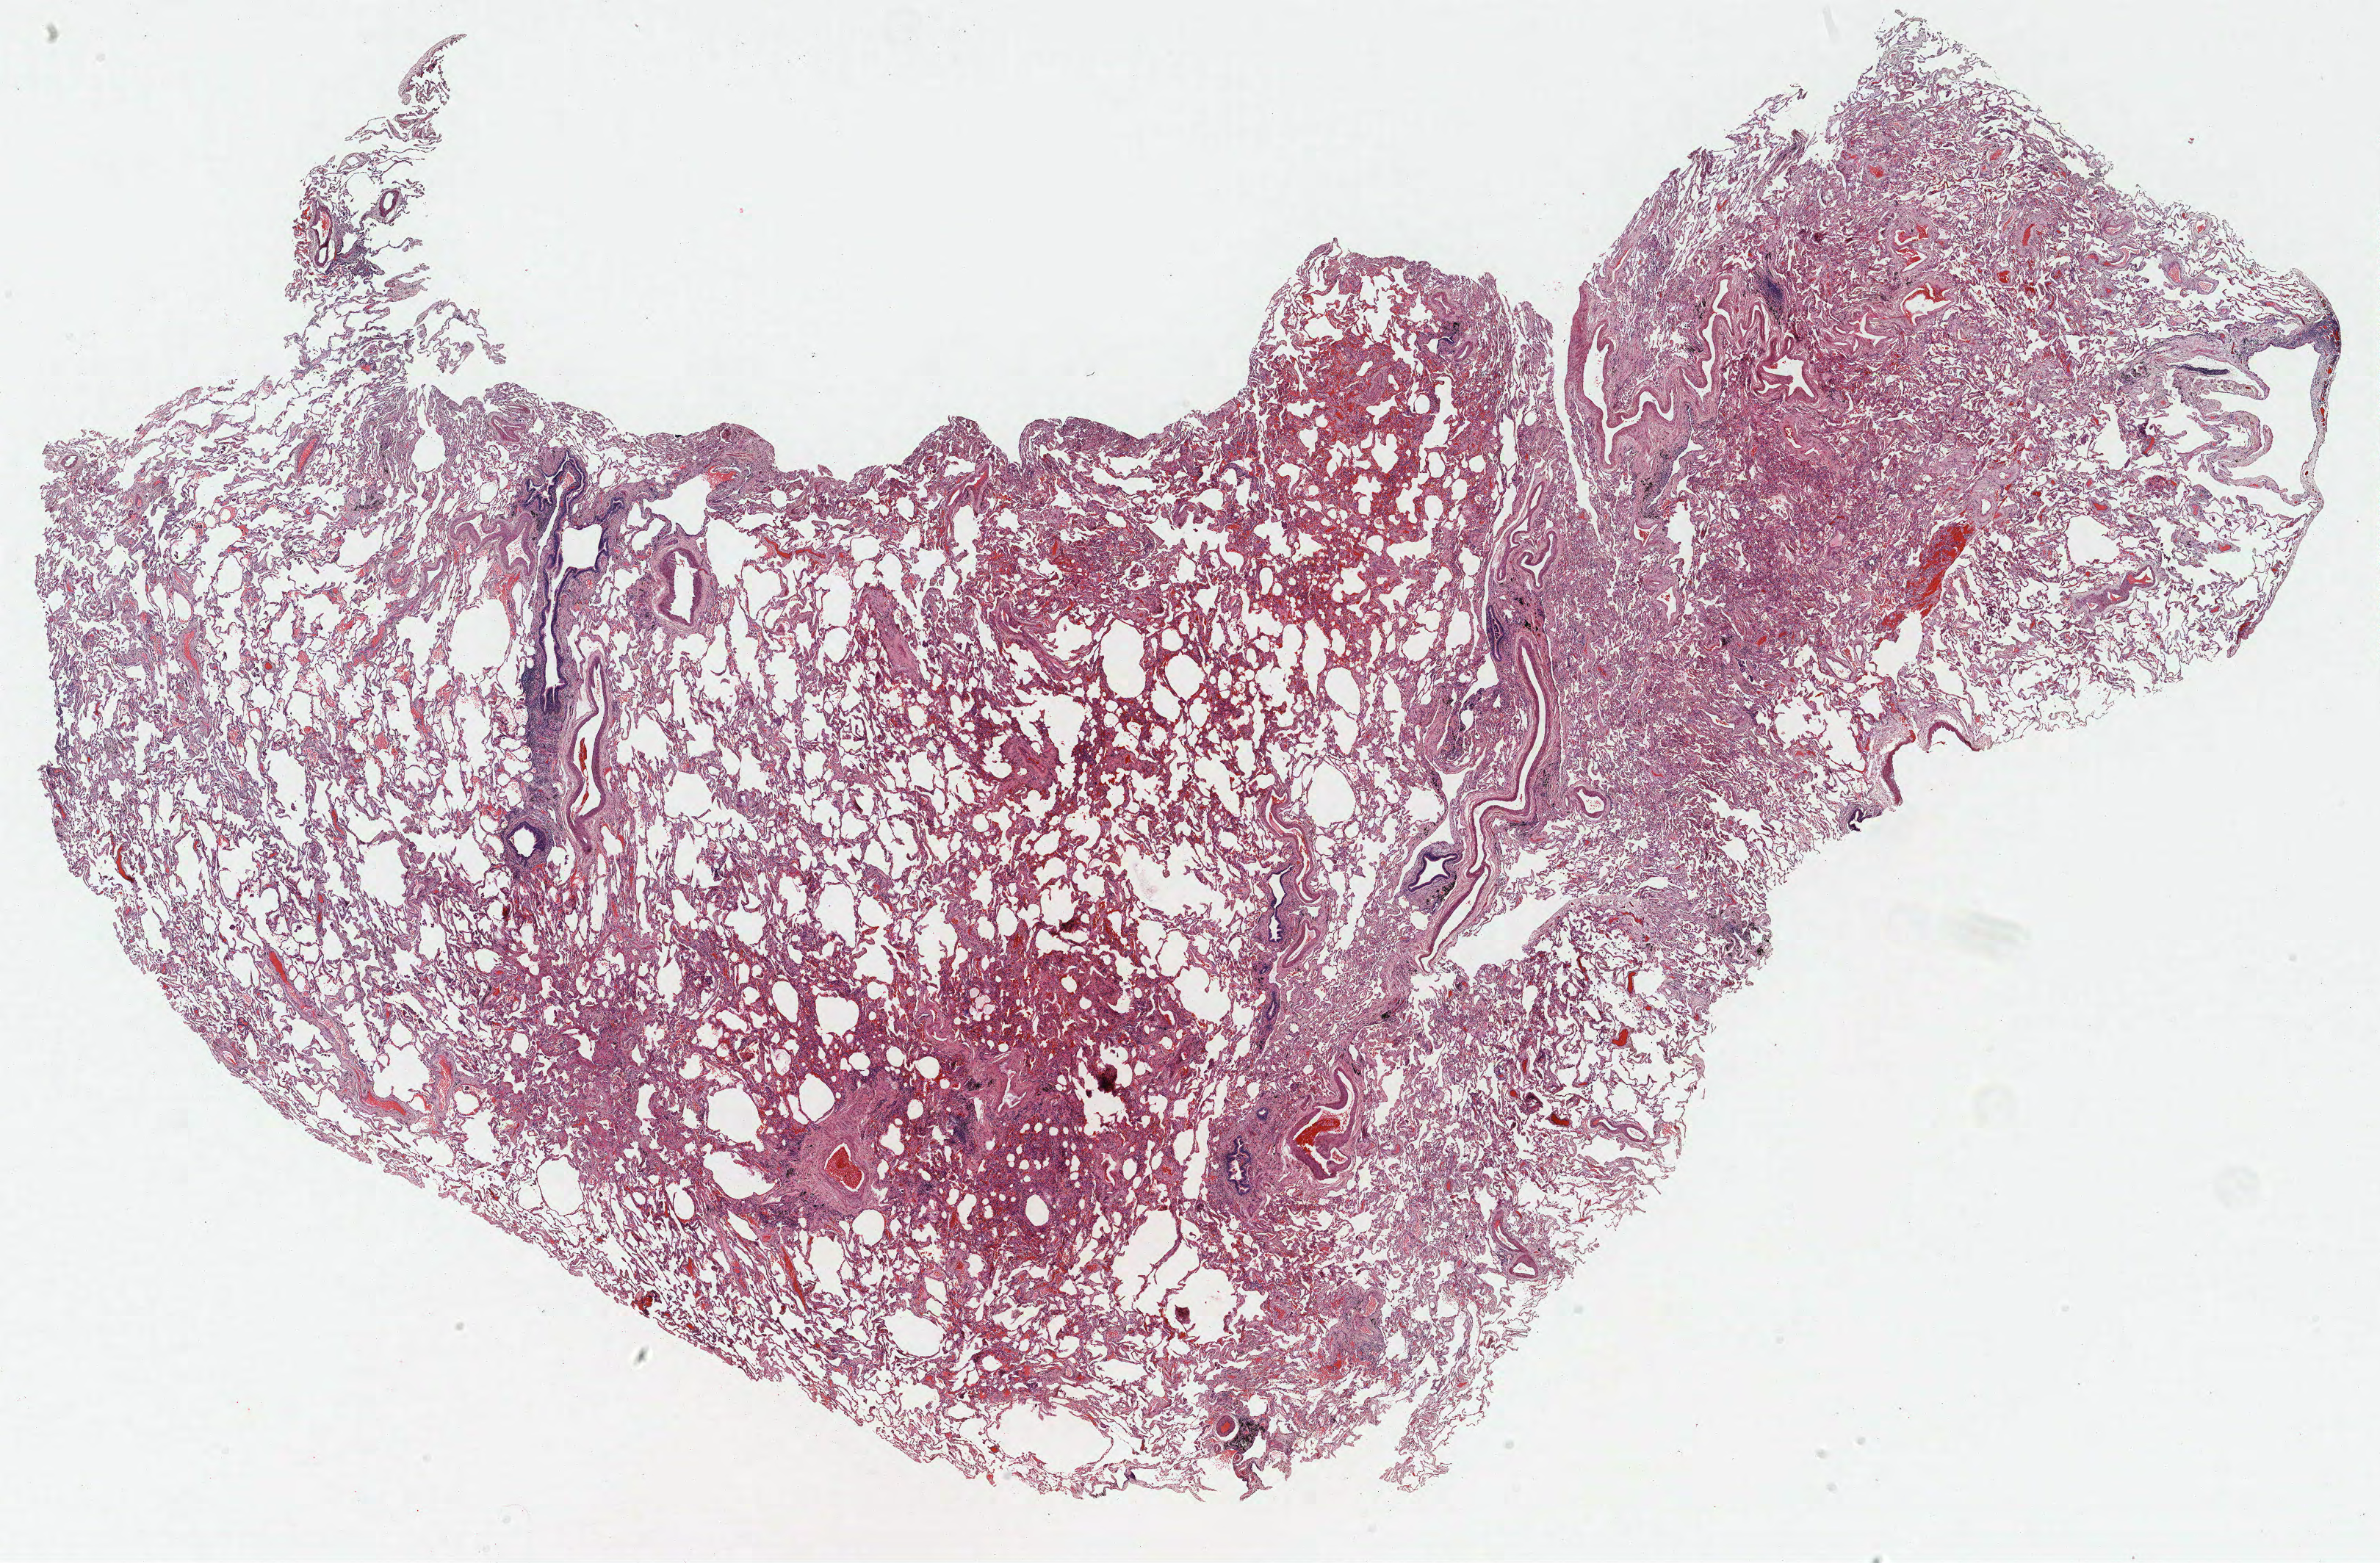
Whole-slide histology image, H&E — a low-resolution overview of the entire scanned area, about 25.9 x 17.0 mm (slide scanned at 40x). FFPE section. Lung tissue. Female, age 64 at enrolment. Current smoker at enrolment. Grade: moderately differentiated (G2).
Stage (AJCC 6th edition): IA. Tumour size (pathology): 15 mm. Participant's lung-cancer diagnosis: Adenocarcinoma, NOS. Primary tumour location (clinical record): right lower lobe.